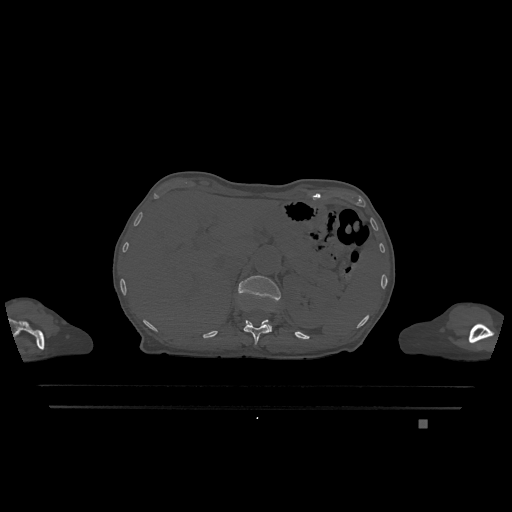
CT including the spine, one axial slice; bone window (W 1800 / L 400 HU); 512 × 512 image matrix, field of view 500 × 500 mm. Patient: female, 74 years. From the clinical record (not read from this slice): primary cancer: lung; vertebrae with lytic lesions (as recorded): T1, T4, T5, T6, L4, L5.
Structures marked on this image (semi-automatic segmentation, software-assisted and operator-edited):
- L1 vertebra: bounding box [x1, y1, x2, y2] px = [238, 275, 281, 331]
- T12 vertebra: [244, 320, 271, 345]